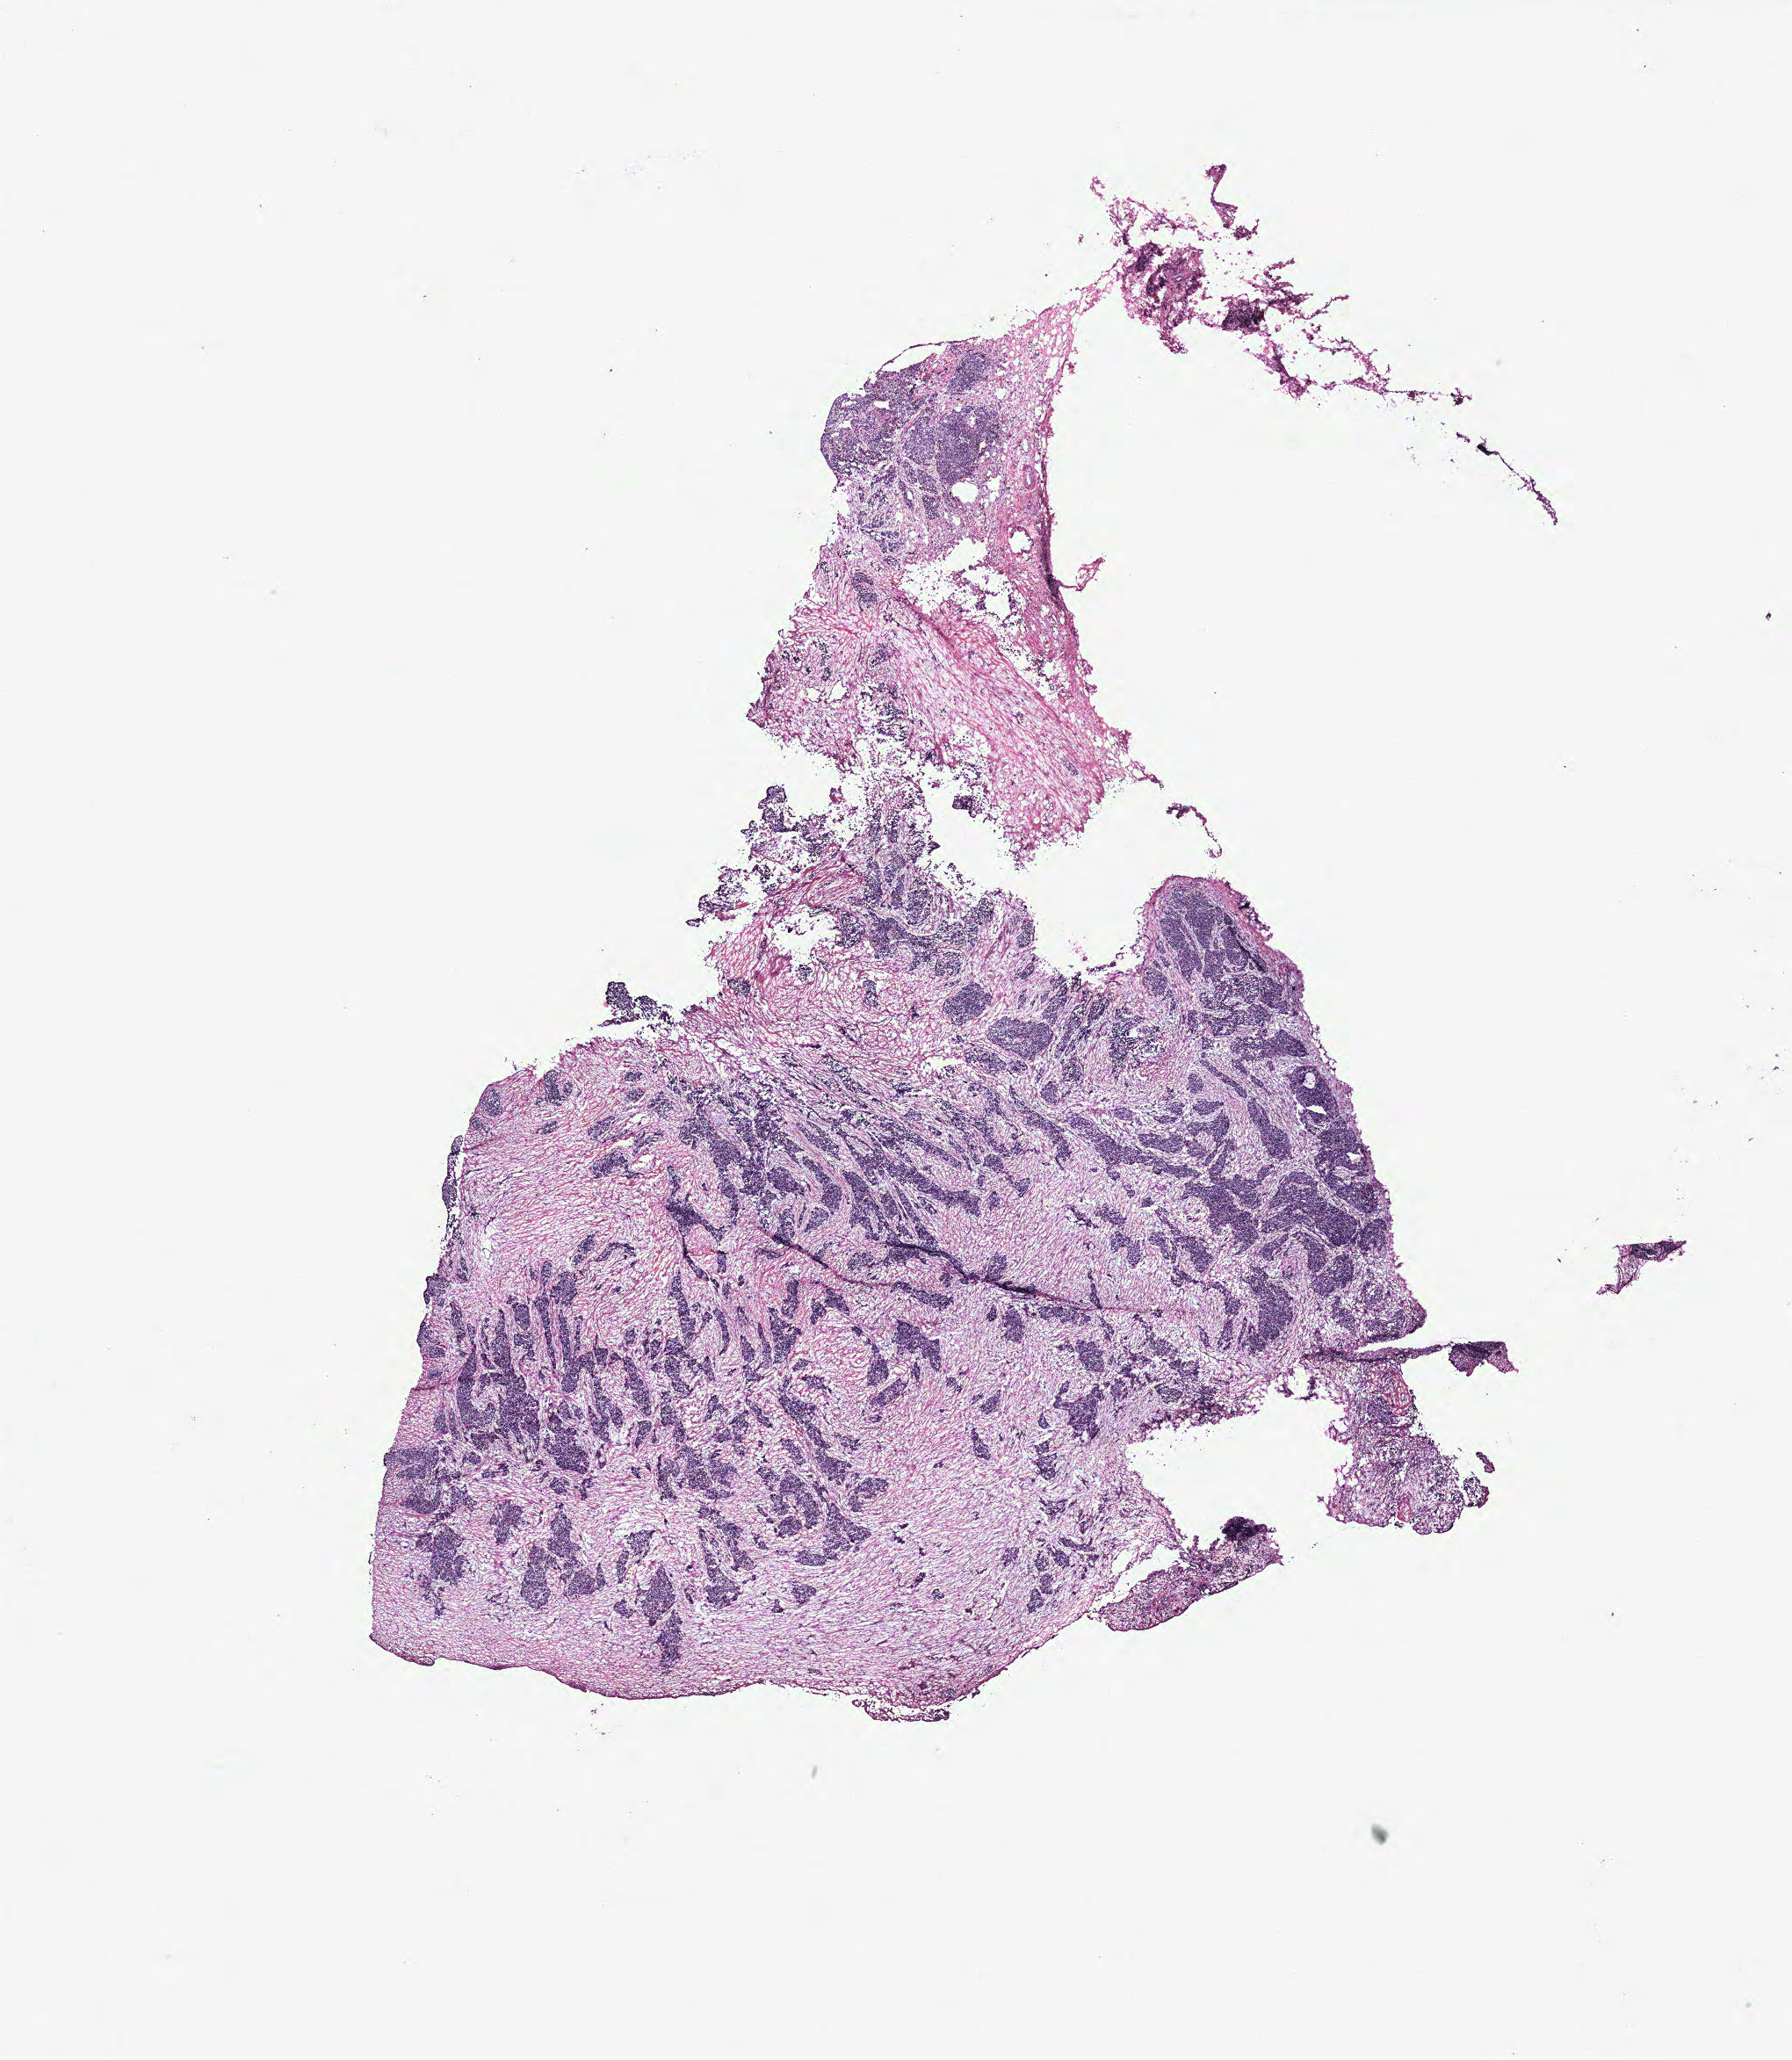
Digitized H&E tissue section (whole slide), low-resolution overview of the scanned area, about 16.3 x 18.8 mm (from a 40x scan), tumour tissue sample, ovary. Female, 70 y/o.
Diagnosis: Serous adenocarcinoma, NOS (peritoneum, NOS). Primary tumour site (as recorded): peritoneum.